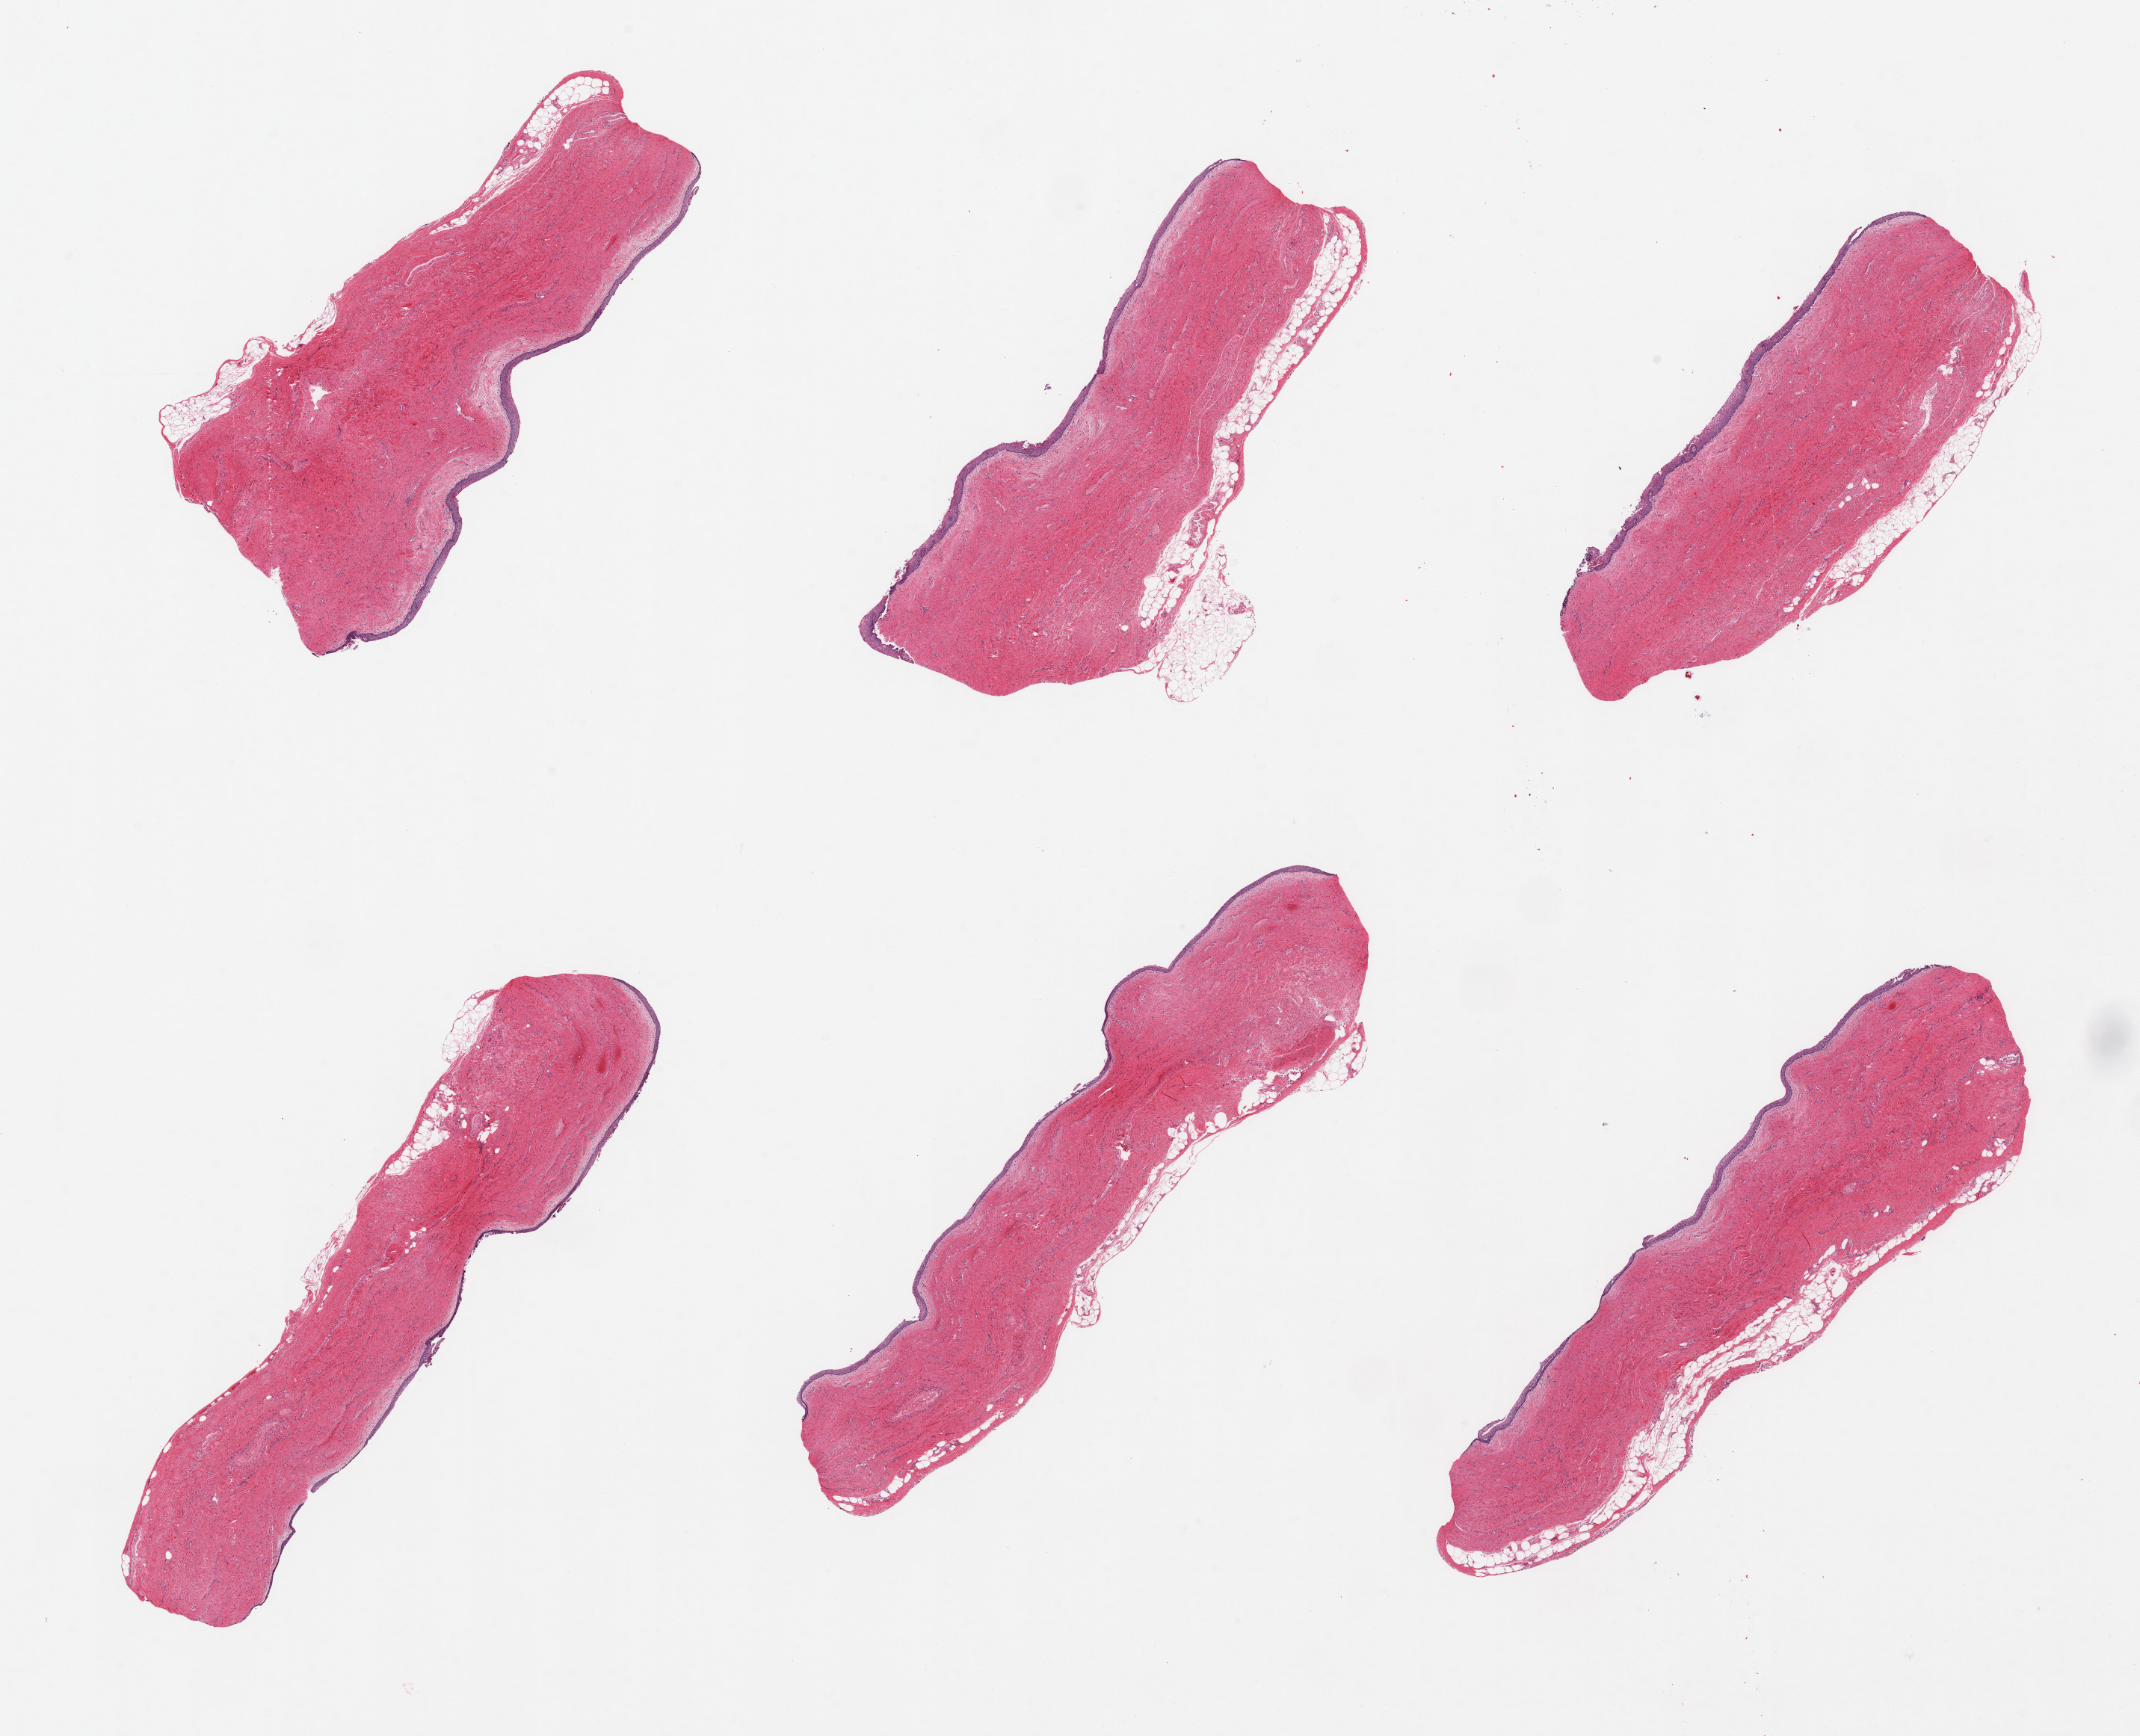
Hematoxylin and eosin (H&E) whole-slide image — low-resolution overview of the scanned area, about 22.6 x 18.4 mm (slide scanned at 20x); PAXgene-fixed paraffin-embedded (PFPE) section; sampled site (target tissue): vagina; donor tissue sample. Donor sex: female.
Reviewer comment on this tissue sample: 6 pieces, squamous epithelium up to ~0.15mm, partially sloughing.